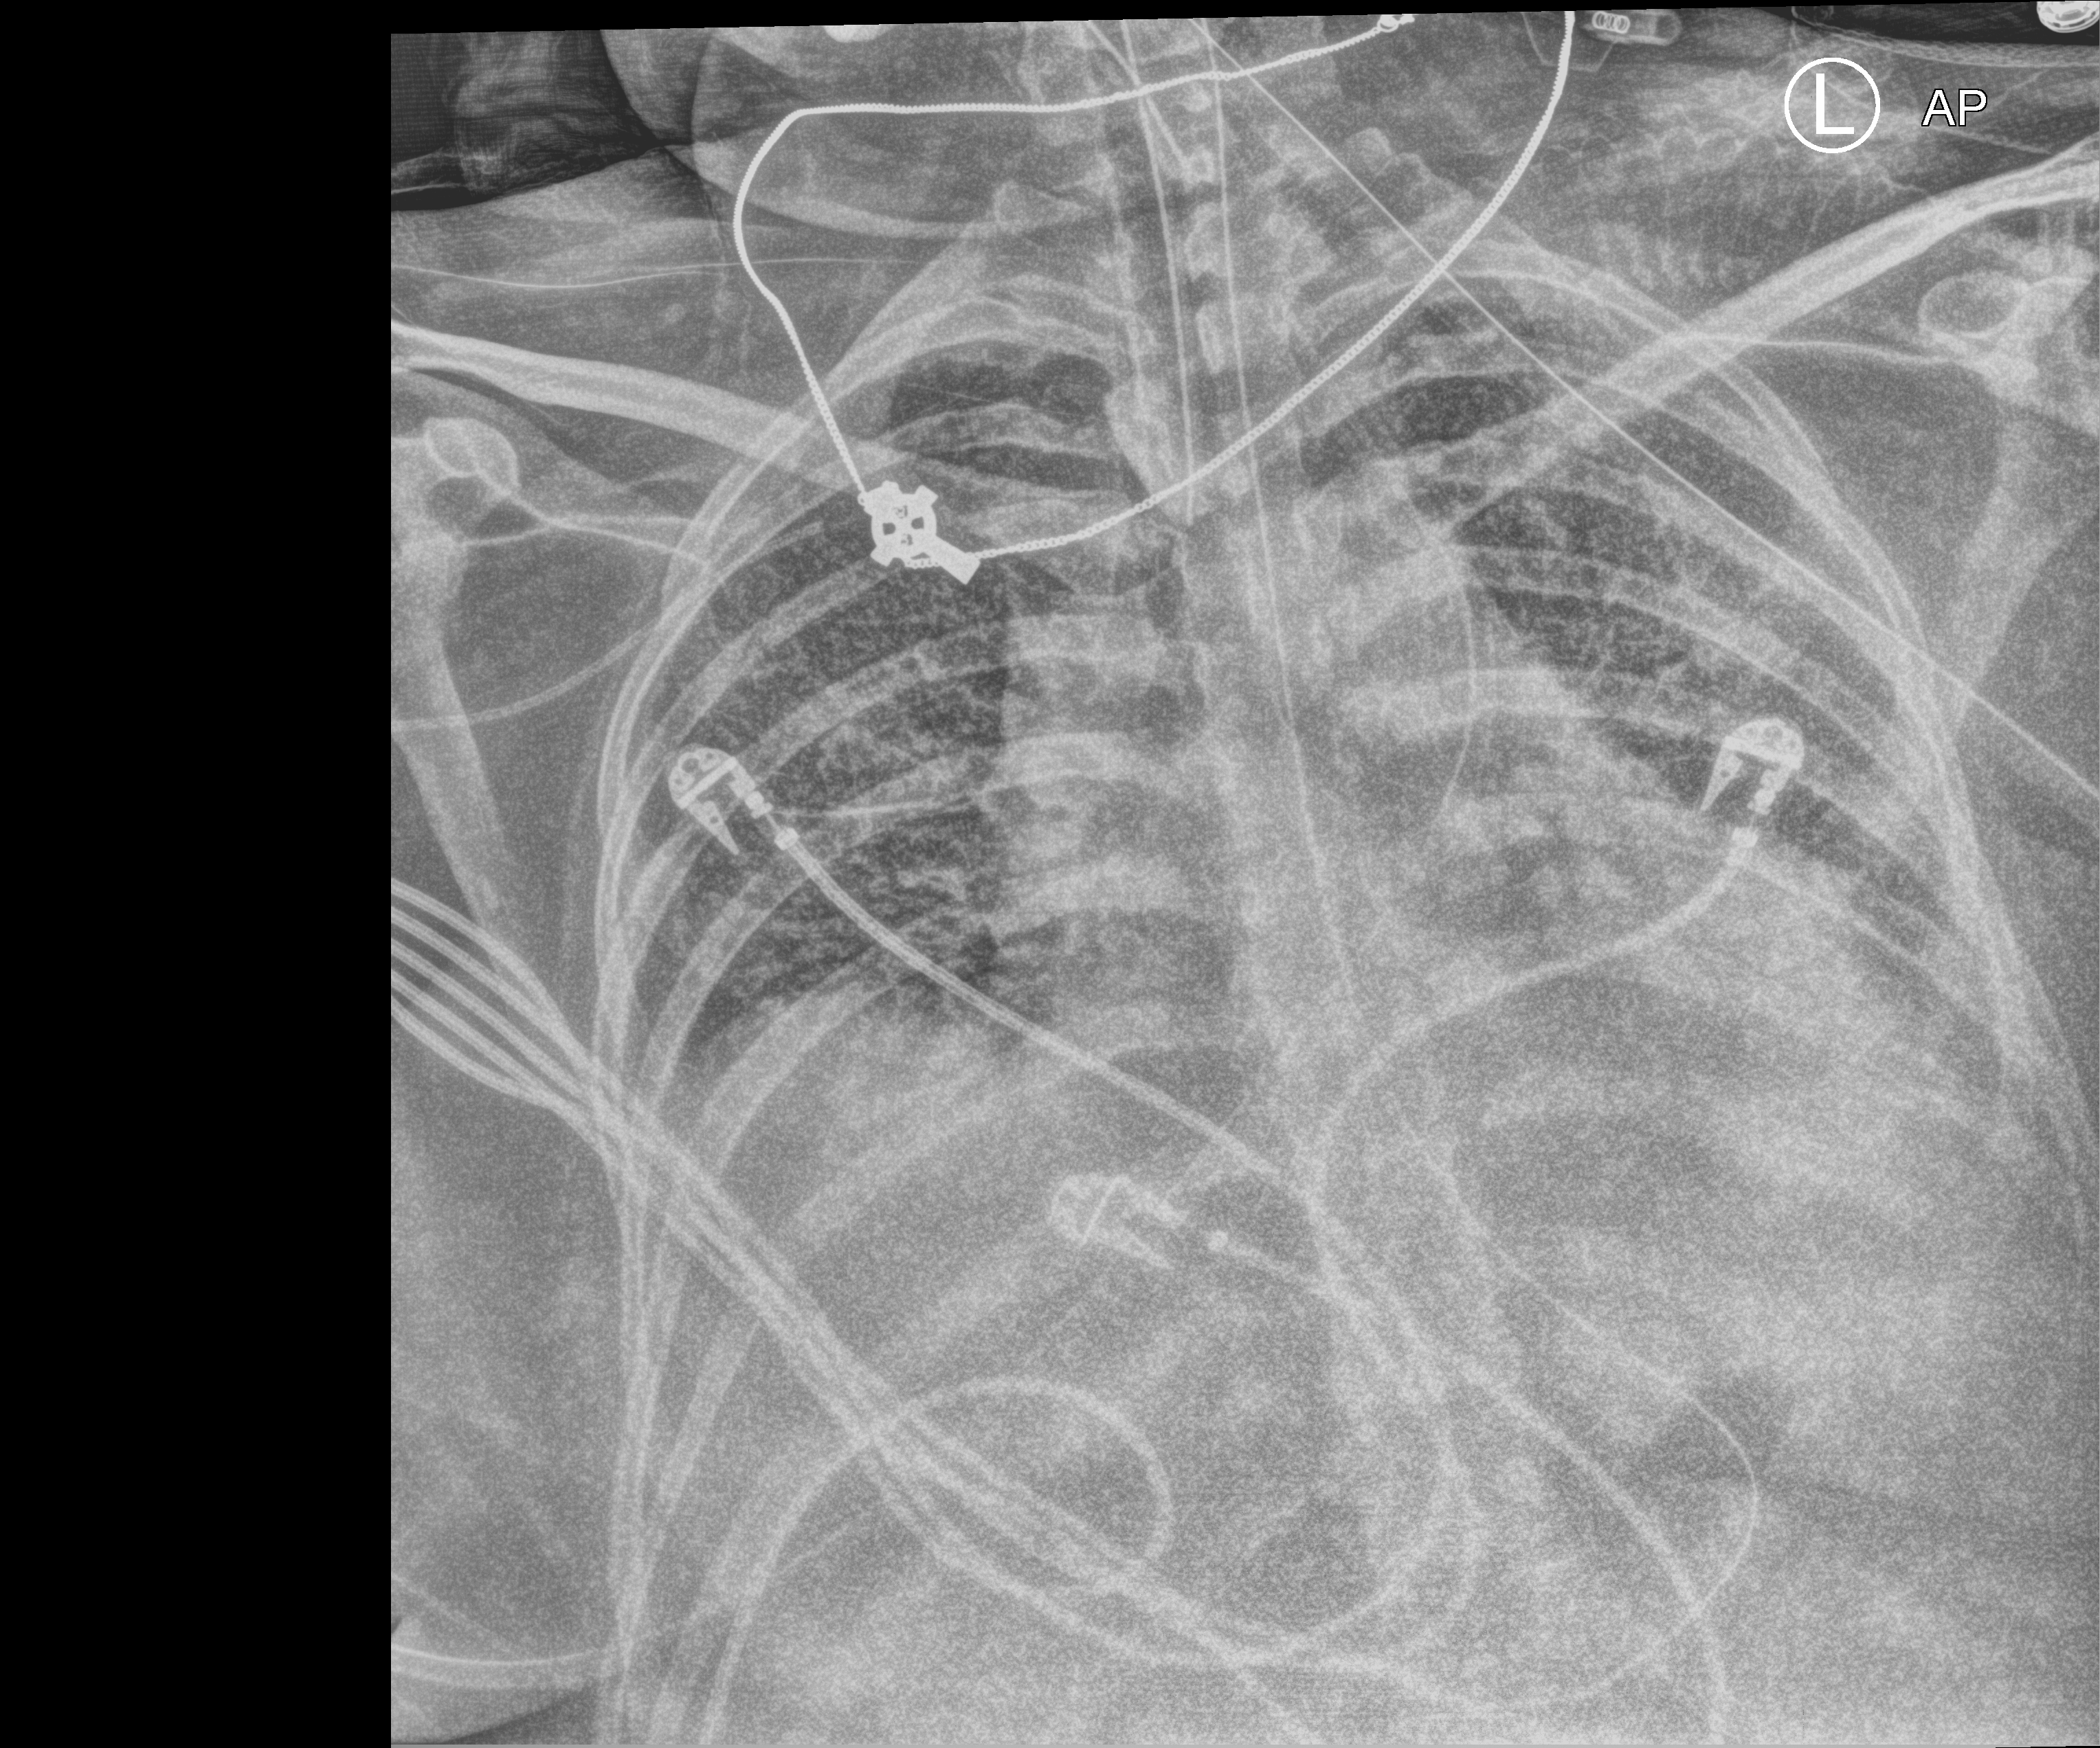
Chest X-ray (portable); anteroposterior (AP) projection. Female patient hospitalised with COVID-19, age 18–59 years.
Hospital-stay facts (about this admission, not read from this image; timing relative to this image not recorded): admitted to intensive care during this hospital stay: yes.